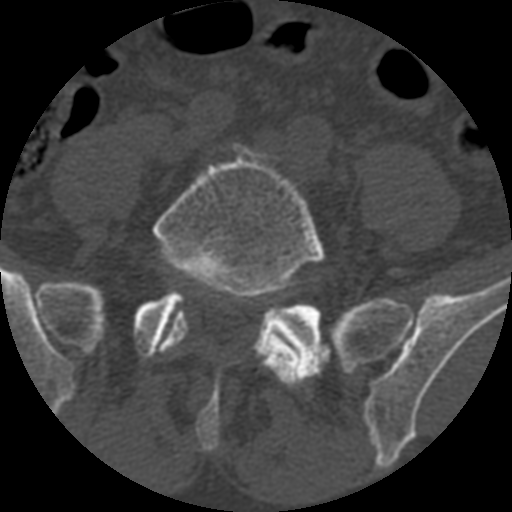
CT including the spine, one axial slice. Position 249 of 399 along the scan axis. 120 kVp. Bone window (W 1800 / L 400 HU). 1.25 mm slice thickness. 512 × 512 image matrix, field of view 160 × 160 mm. Patient age 71 years. Case-level facts recorded for this patient, not image findings: primary cancer: prostate.
Outlined on this slice (semi-automatically segmented with operator editing):
- L5 vertebra: bounding box [x1, y1, x2, y2] px = [152, 143, 328, 387]